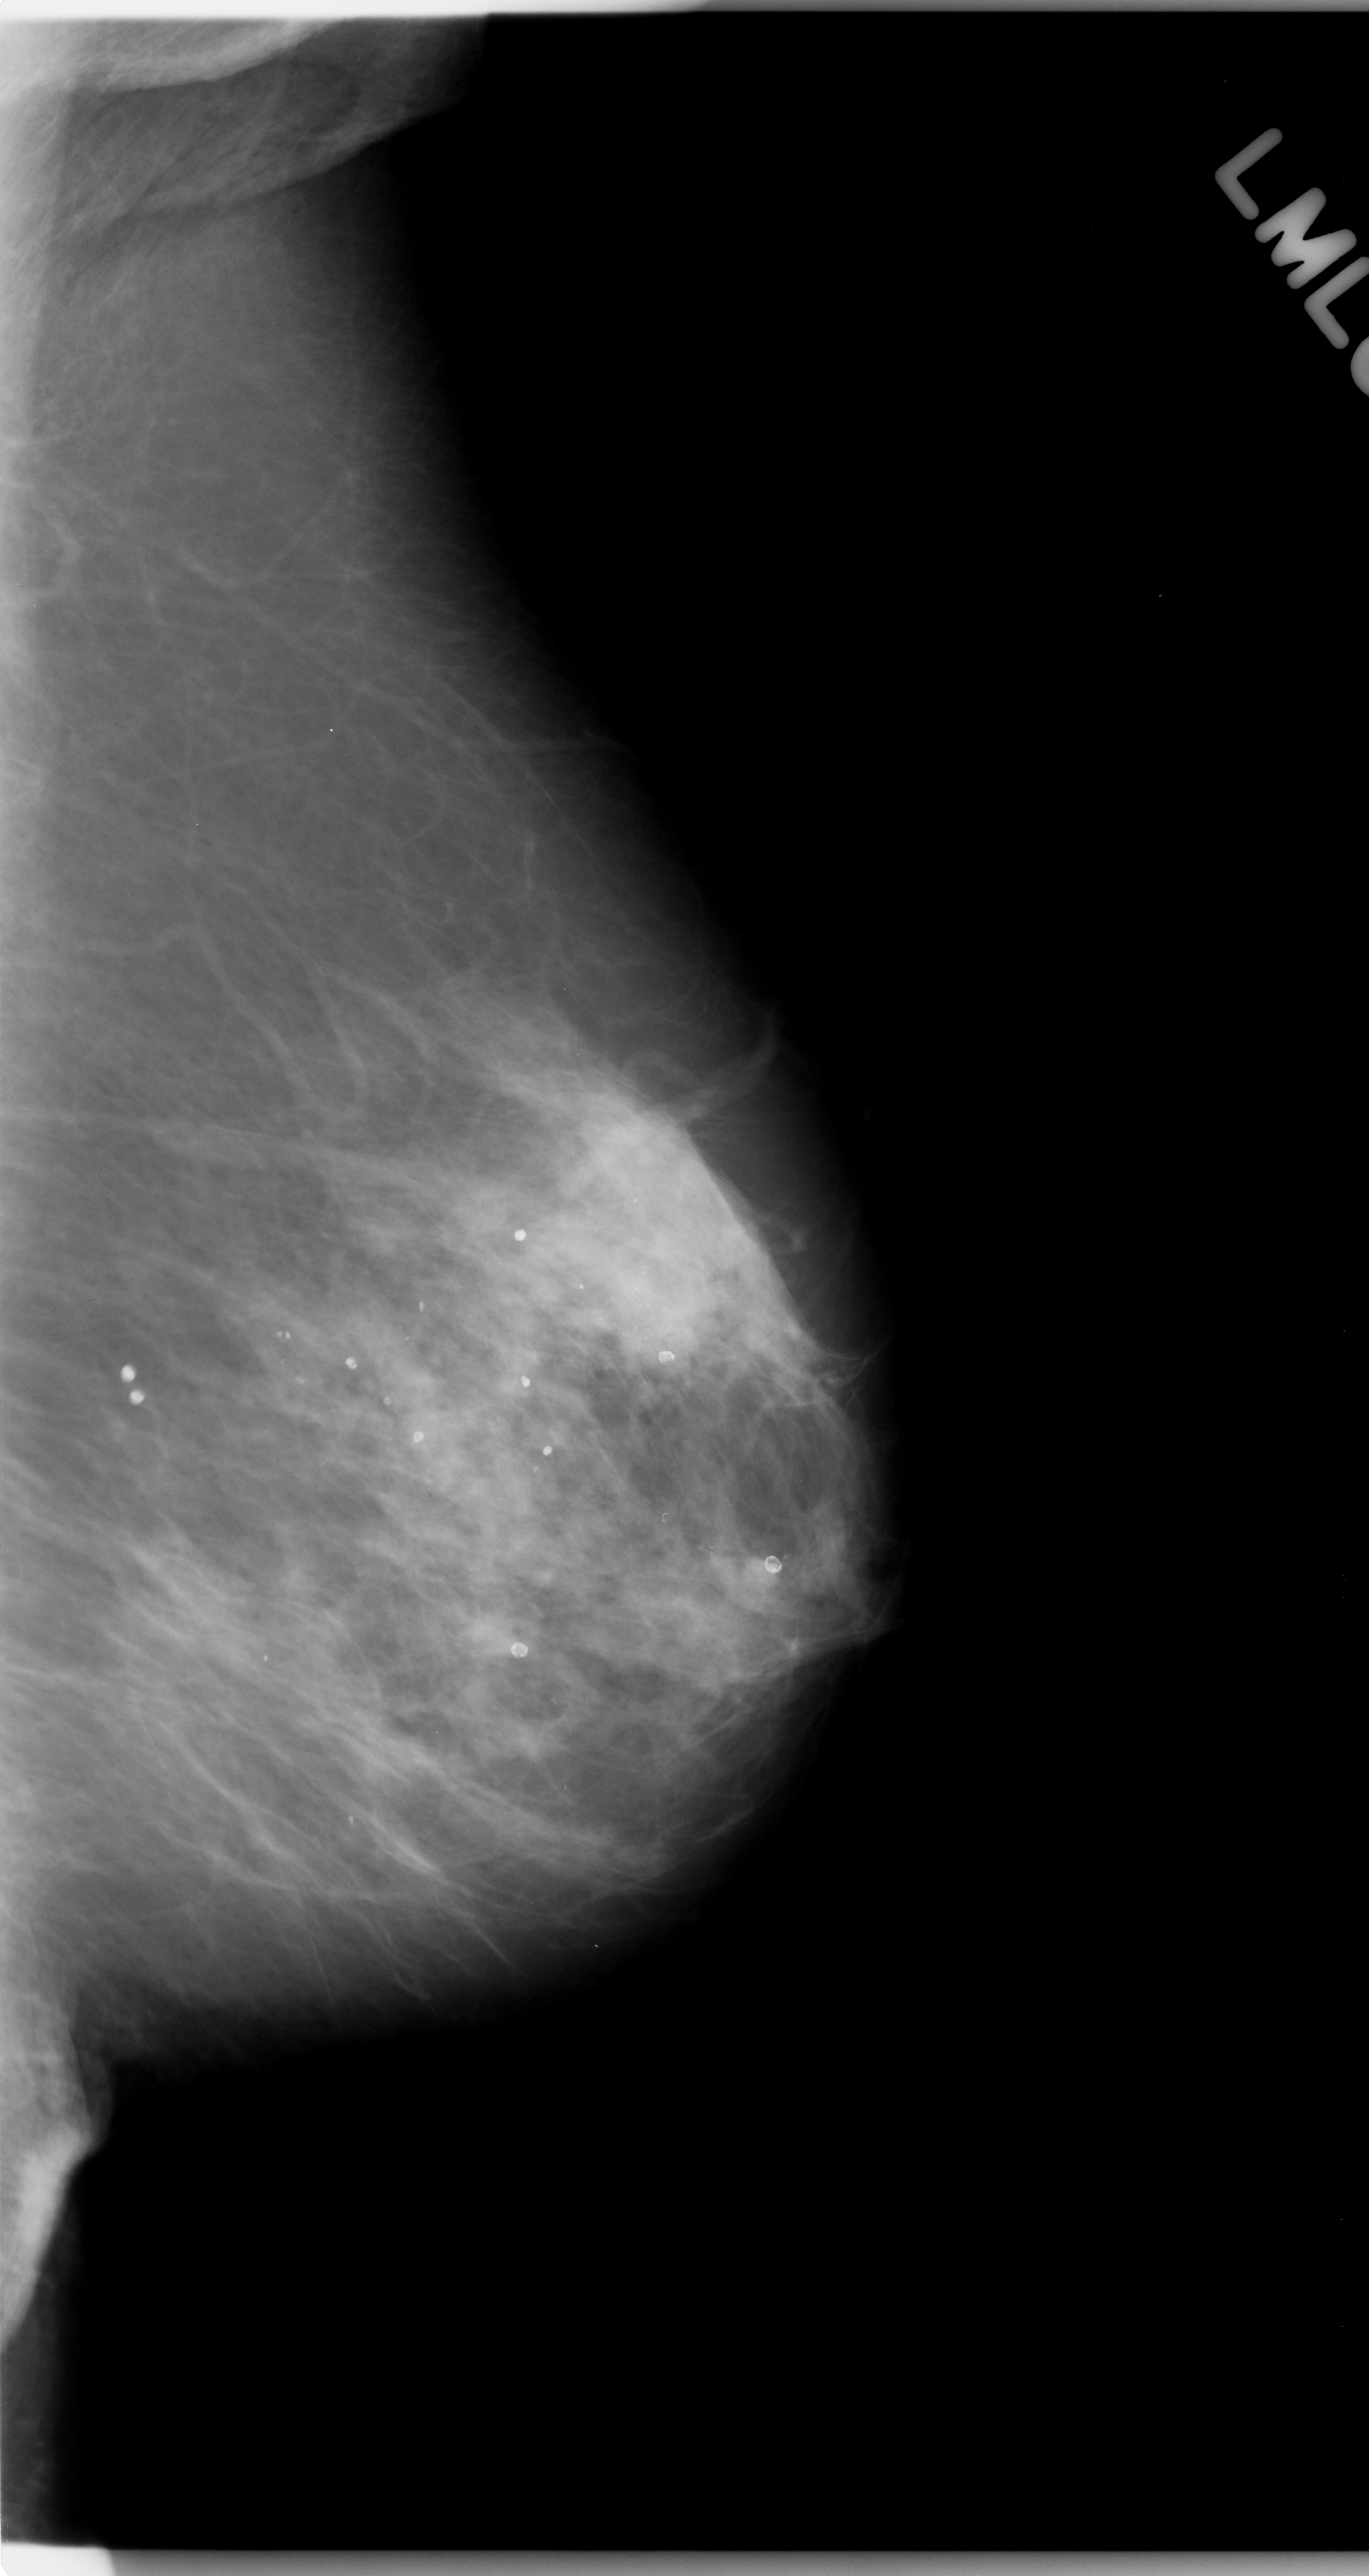
Scanned film-screen mammogram. Left breast. Mediolateral oblique (MLO) view. BI-RADS breast density category 2 (scale 1–4). 1369 × 2576 image matrix.
Expert-marked regions of interest on this image (one box per marked abnormality):
- calcifications, morphology amorphous, distribution clustered; BI-RADS assessment category 5; subtlety rating 4 on a 1 (subtle) to 5 (obvious) scale; pathology result (as recorded, not read from the image): malignant: box from (x=575, y=1217) to (x=735, y=1388) px